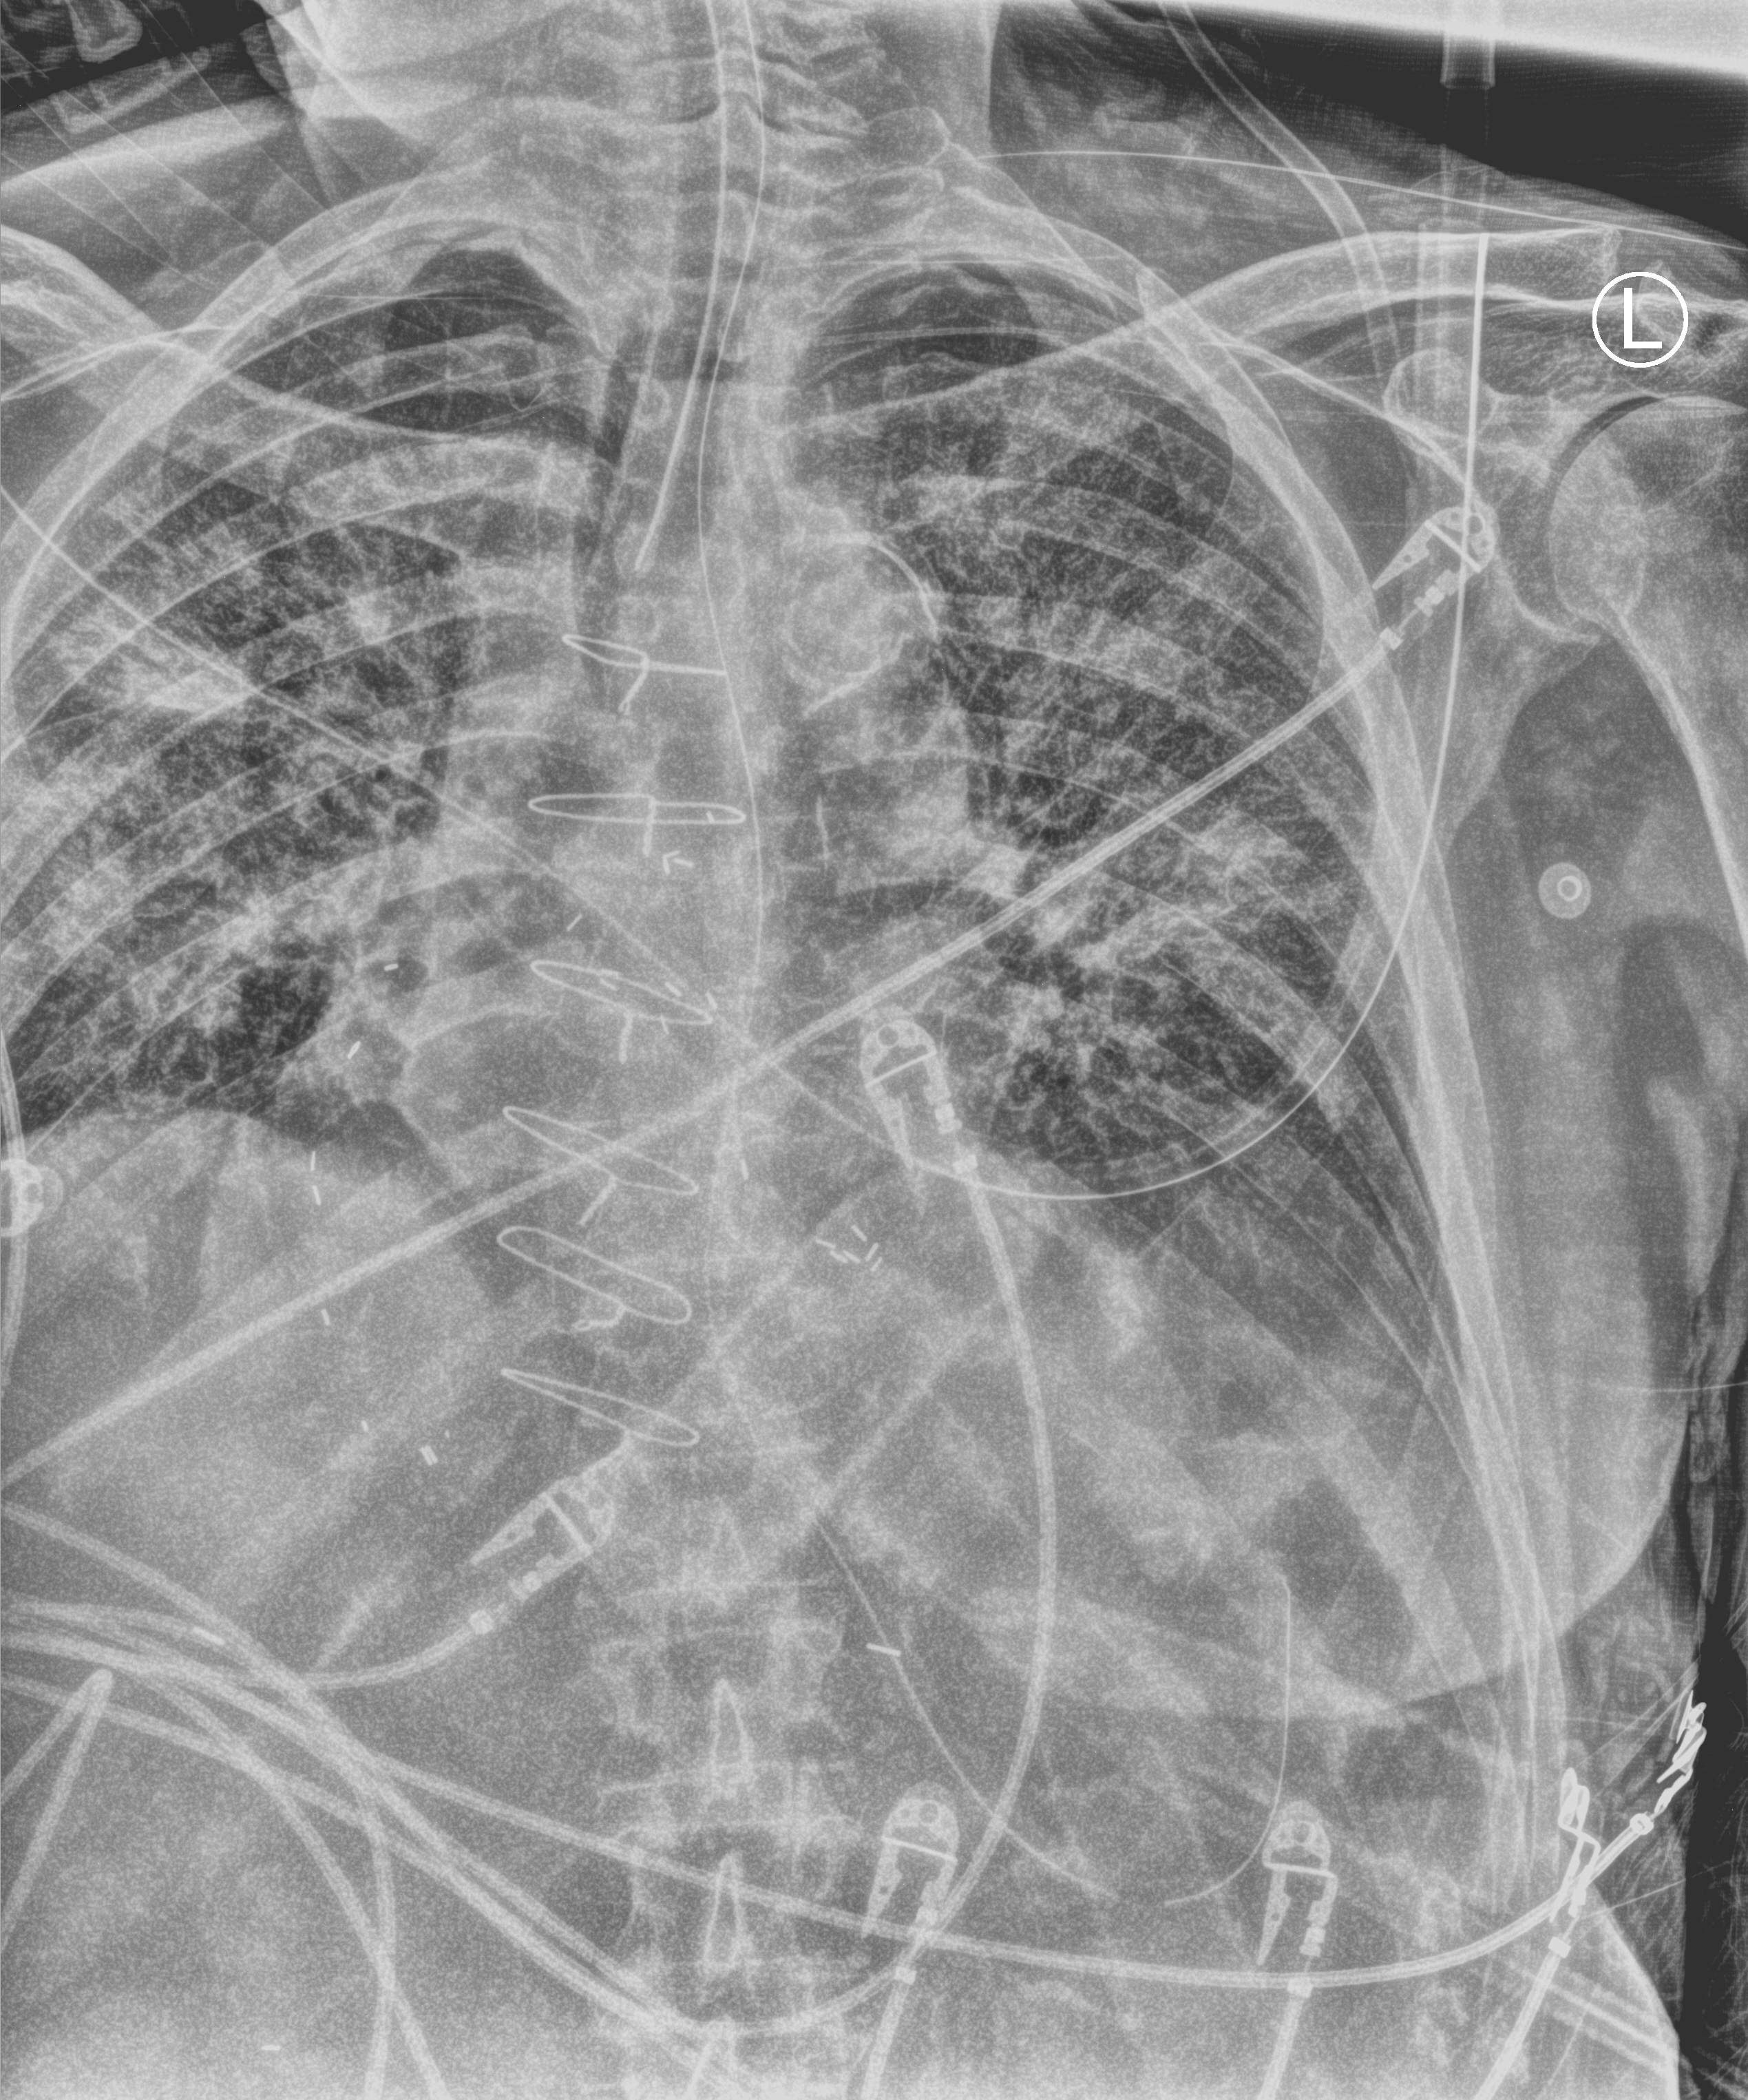
Chest X-ray (portable). Patient hospitalised with COVID-19; male, aged 75–90 years.
Hospital-stay facts (about this admission, not read from this image; timing relative to this image not recorded): smoking status (admission record): never.